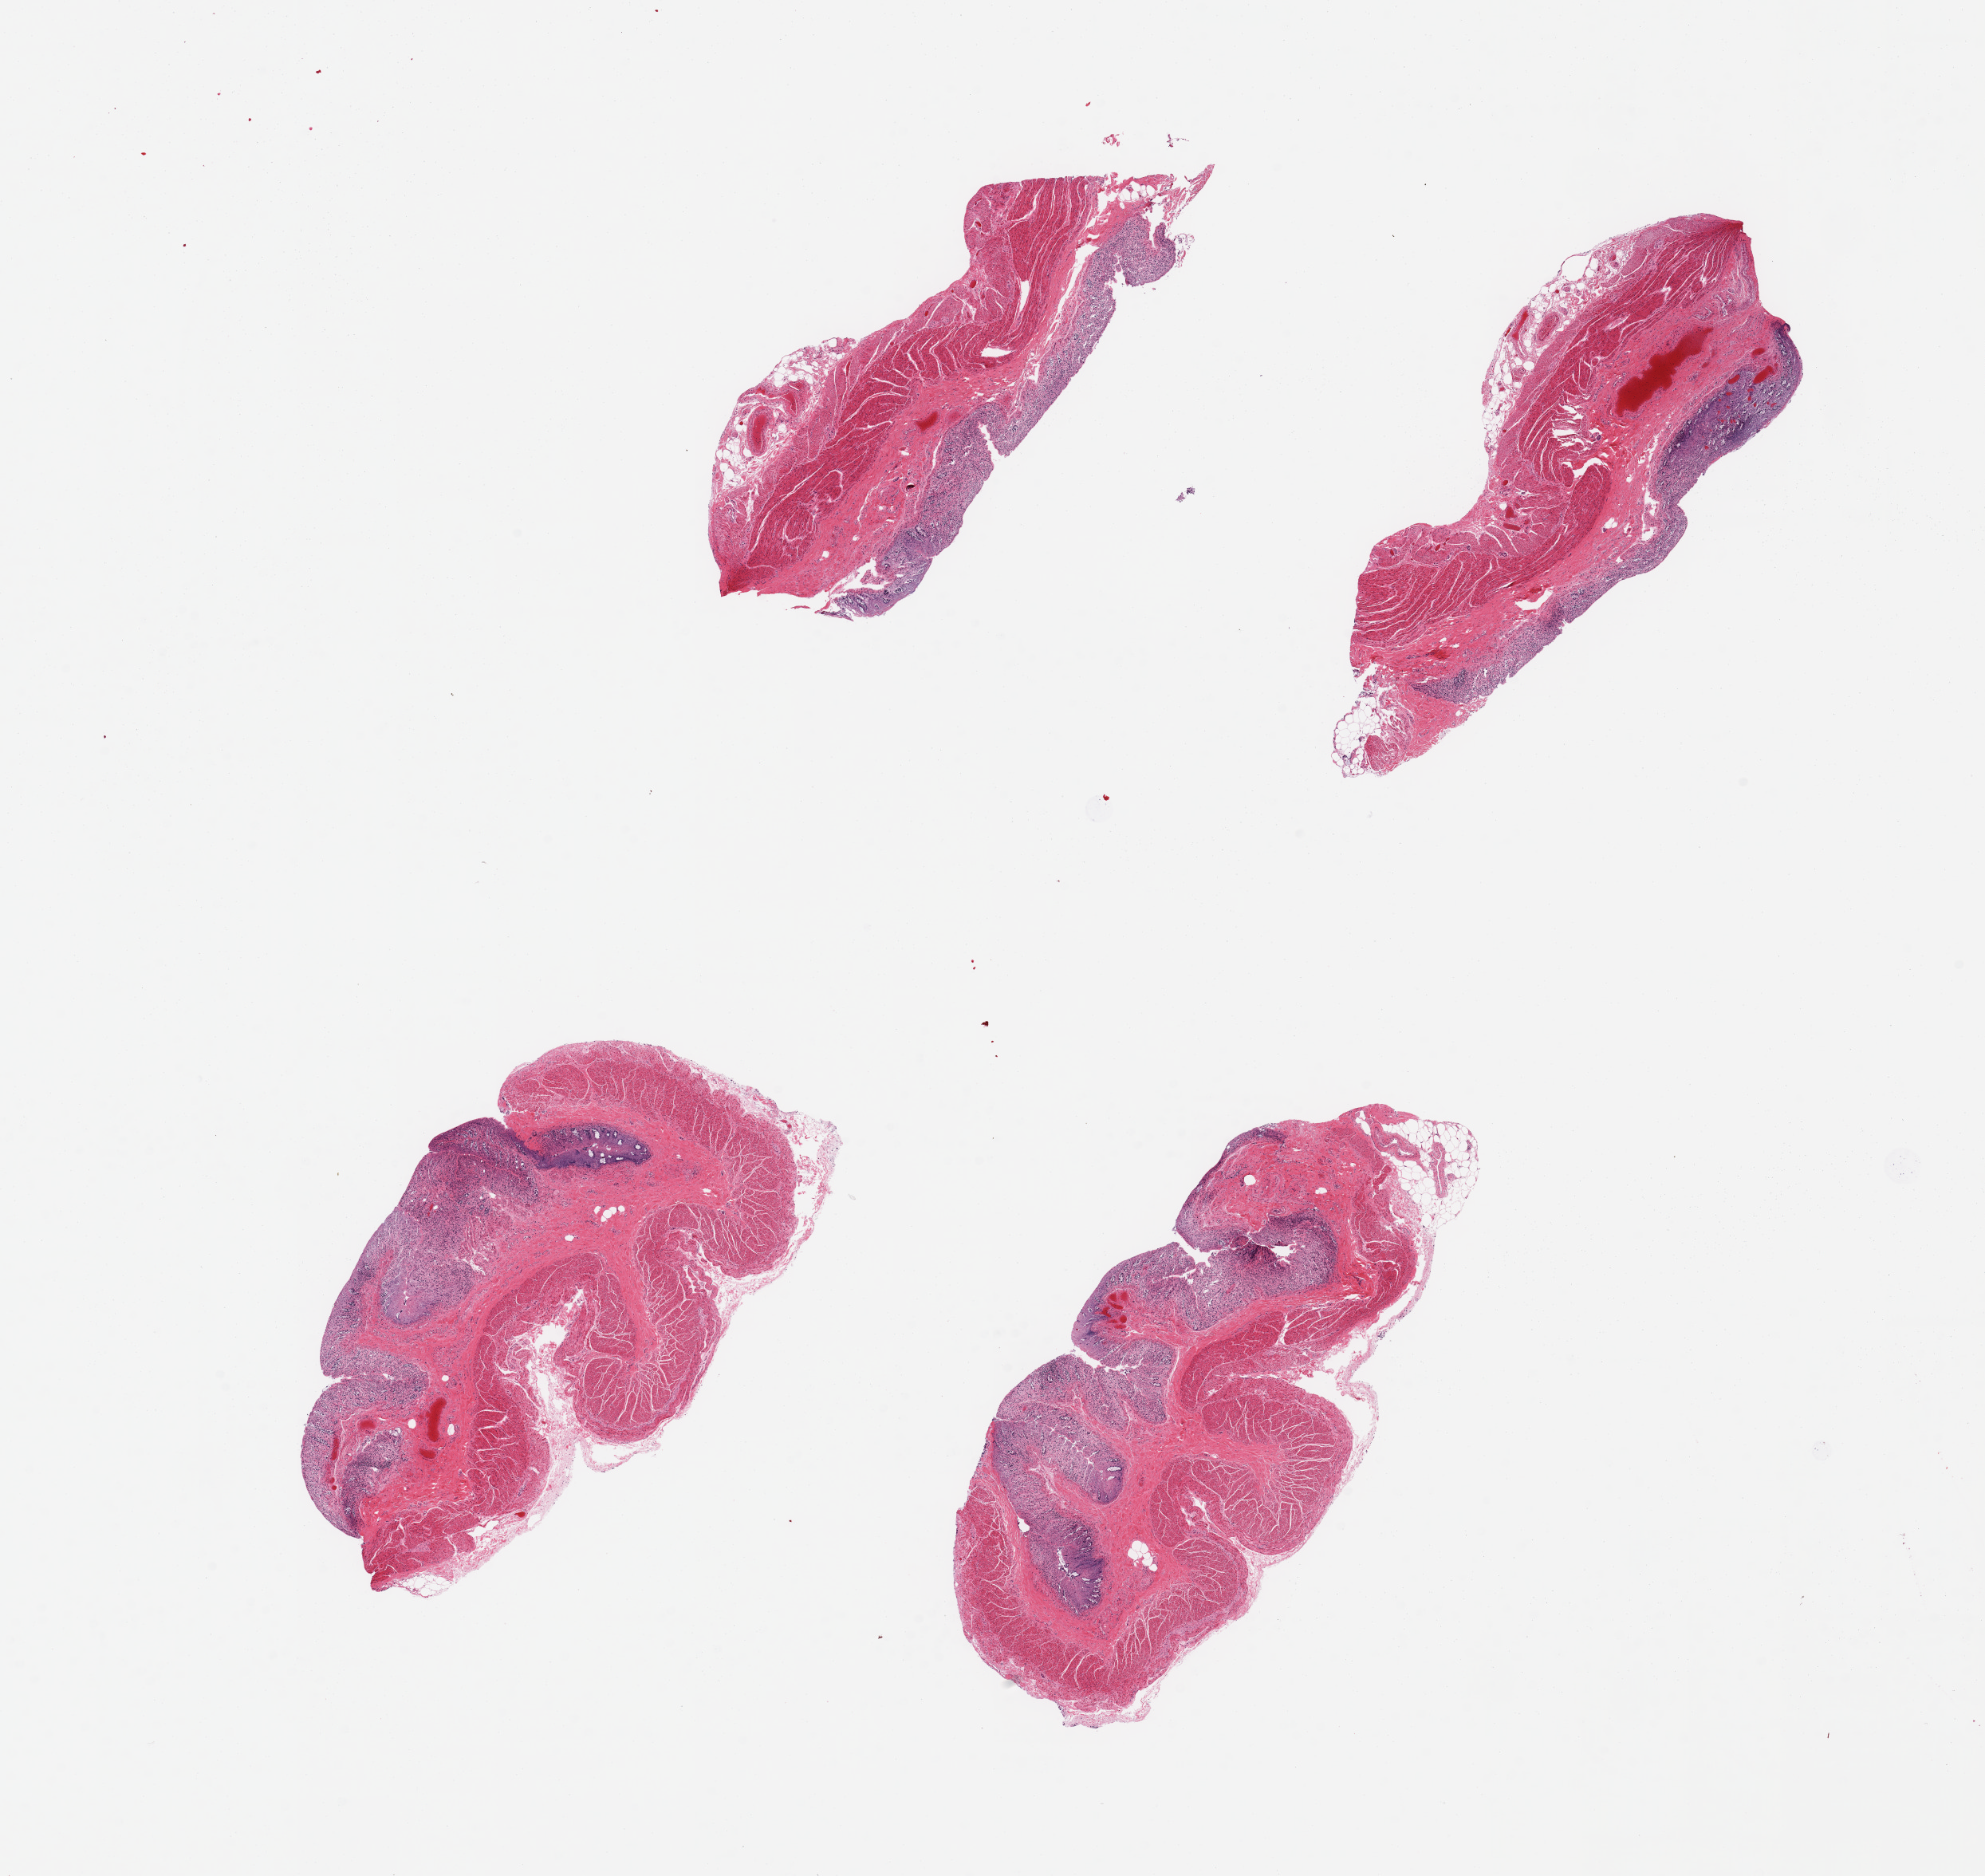
Whole-slide image, haematoxylin and eosin stain — low-resolution overview of the scanned area, about 19.7 x 18.6 mm. PAXgene-fixed, paraffin-embedded tissue. Sampled site (target tissue): transverse colon. Donor tissue sample. Donor: male.
• reviewer comment on this tissue sample: 4 pieces, mucosa up to ~0.6mm, glandular mucosa autolyzed, mainly lamina propria